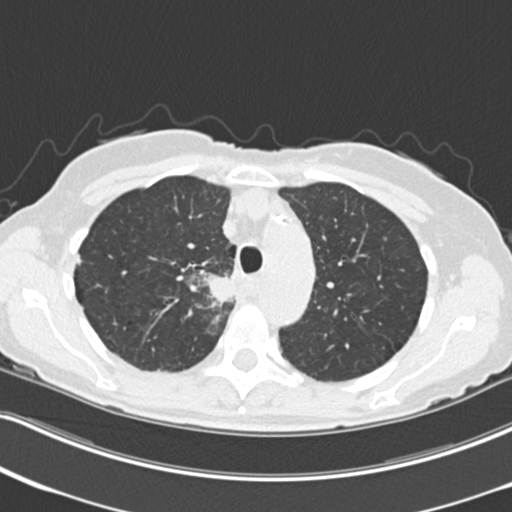
Low-dose screening chest CT, one axial slice. Slice 169 of 226 in the series (ordered by position). Lung window (W 1500 / L -600 HU). 512 × 512 image matrix, field of view 322 × 322 mm.
Outlined on this slice (outlined manually by an expert reader):
- lesion 1 (tumor, mediastinum): bounding box <208,274,234,304> (left, top, right, bottom; pixels)